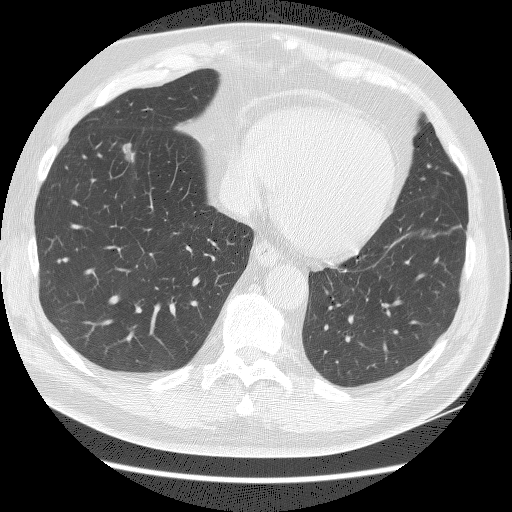
Axial slice from a low-dose chest CT screening exam, first (baseline) screen, lung window (W 1500 / L -600 HU), lung (sharp) reconstruction kernel (BONE), 512 × 512 image matrix. Male participant, aged 65 years at enrolment.
Expert reader's lesion annotation, box from (x=106, y=133) to (x=151, y=169) px. The screening reader recorded 3 non-calcified nodules or masses ≥4 mm on this exam; which of them this box marks is not recorded. Lung cancer was diagnosed 132 days after this screen: adenocarcinoma, NOS, right lower lobe, poorly differentiated (G3), stage IA (AJCC 6th edition), 10 mm at pathology.